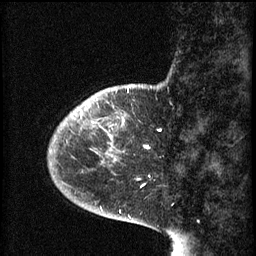
Breast MRI (dynamic contrast-enhanced), one sagittal slice; position 11 of 60 along the scan axis; 3 images stored at this slice position (order not interpretable as contrast timing); 1.5 T; TE 4.2 ms, TR 8.1 ms; 2 mm slice thickness; 256 × 256 image matrix. Female patient, age 44 years.
Outlined on this slice (semi-automatic segmentation, software-assisted and operator-edited):
- analysis volume of interest (the breast-tissue region the enhancement analysis was run in; not a lesion): bounding box [x1, y1, x2, y2] px = [59, 110, 125, 163]
- tumour enhancement mask (voxels above the 70 % enhancement threshold inside the analysis volume of interest): [73, 110, 124, 151]